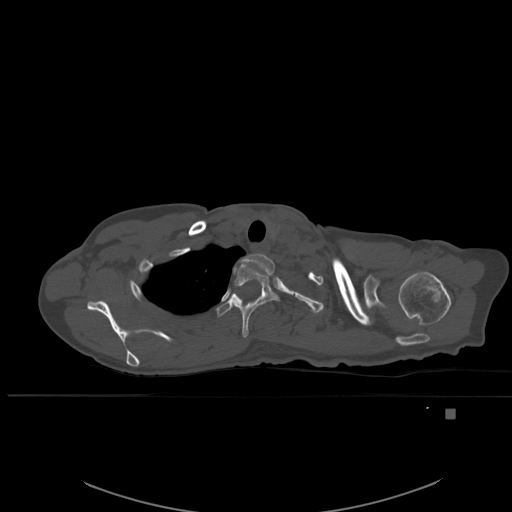
CT including the spine, one axial slice. Bone window (W 1800 / L 400 HU). 512 × 512 image matrix, field of view 440 × 440 mm. Female patient, age 45 years. From the clinical record (not read from this slice): primary cancer: lung.
Annotated regions visible in this slice (semi-automatically segmented with operator editing):
- T1 vertebra: bounding box [x1, y1, x2, y2] px = [235, 254, 275, 275]
- T2 vertebra: [230, 262, 280, 338]
- T3 vertebra: [217, 293, 240, 317]